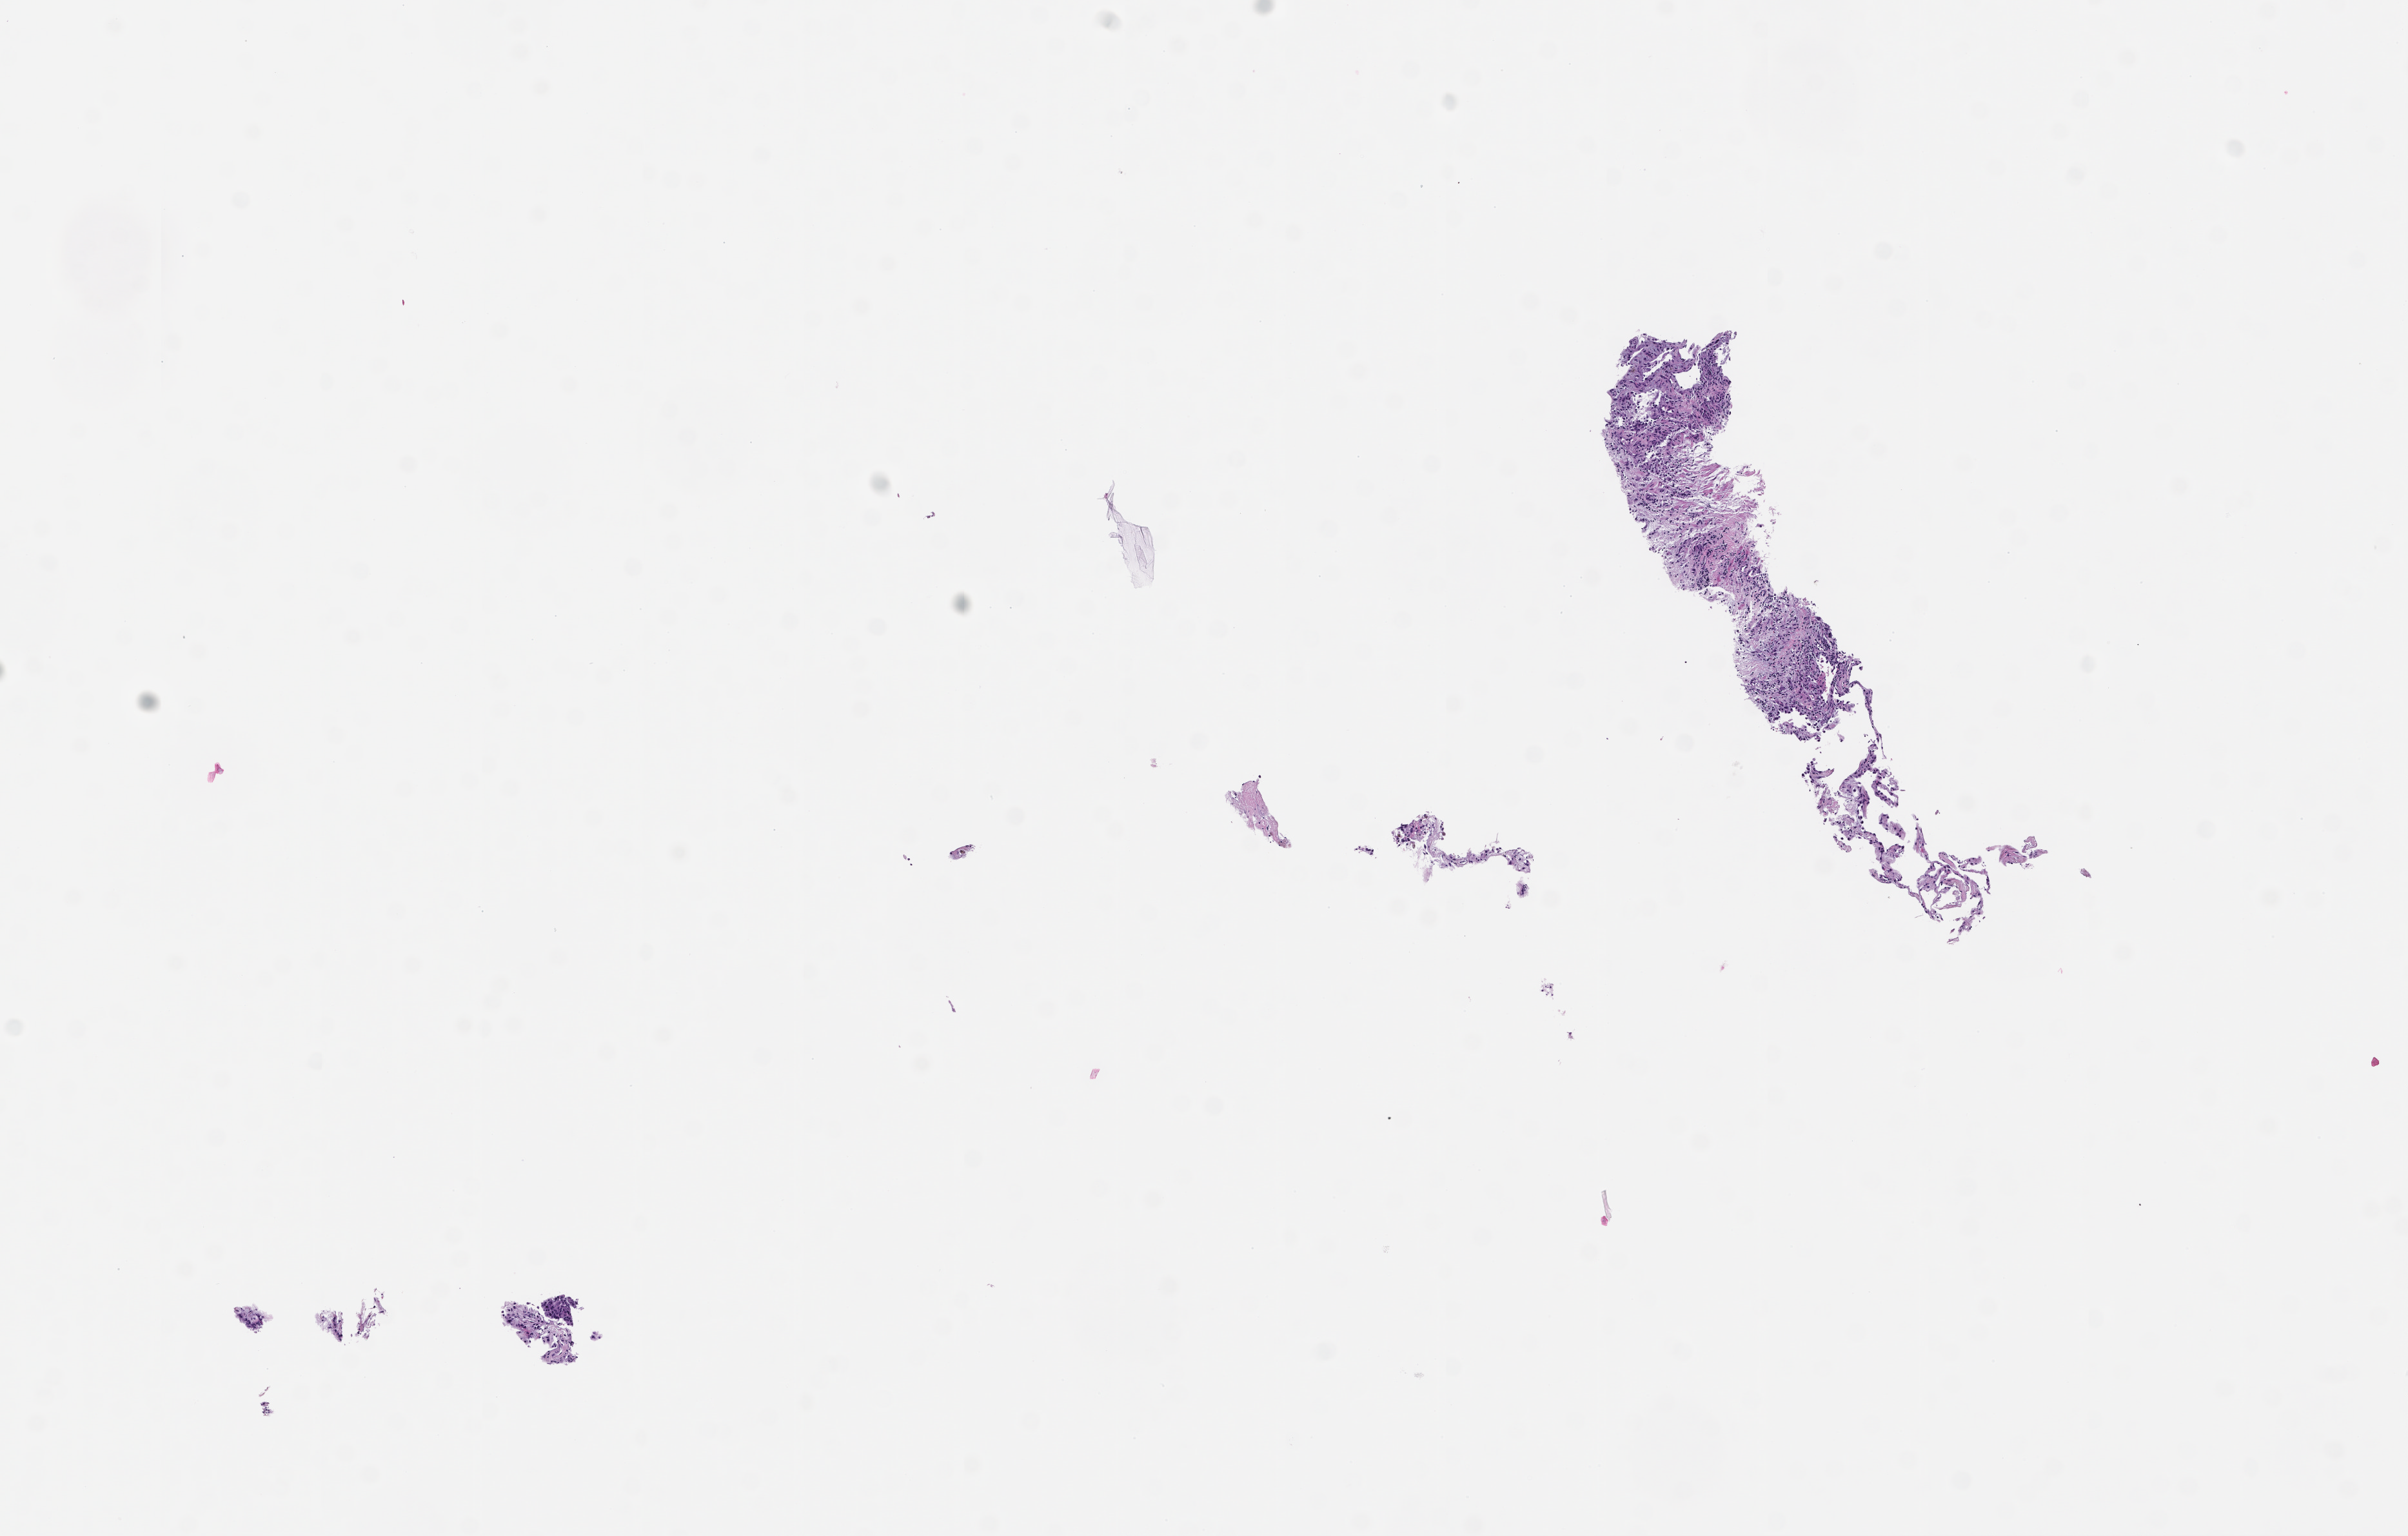
Digitized H&E-stained section, a low-resolution overview of the entire scanned area, about 7.5 x 4.8 mm; formalin-fixed paraffin-embedded section; tissue site: lung; archival tissue. Patient: male.
This section: primary tumor. Diagnosis: Non-Small Cell Lung Carcinoma.